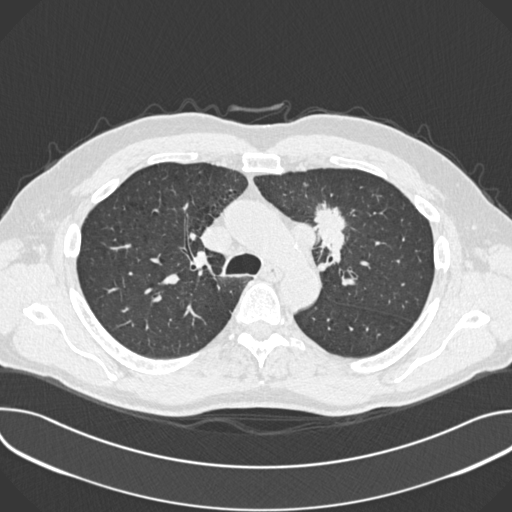
Low-dose screening chest CT, one axial slice; position 260 of 361 along the scan axis; reconstruction kernel B30f; 120 kVp; lung window (W 1500 / L -600 HU); 512 × 512 image matrix, field of view 380 × 380 mm.
Annotated regions visible in this slice (expert manual segmentation):
- lesion 1 (tumor, upper lobe of left lung): box from (x=315, y=207) to (x=346, y=248) px